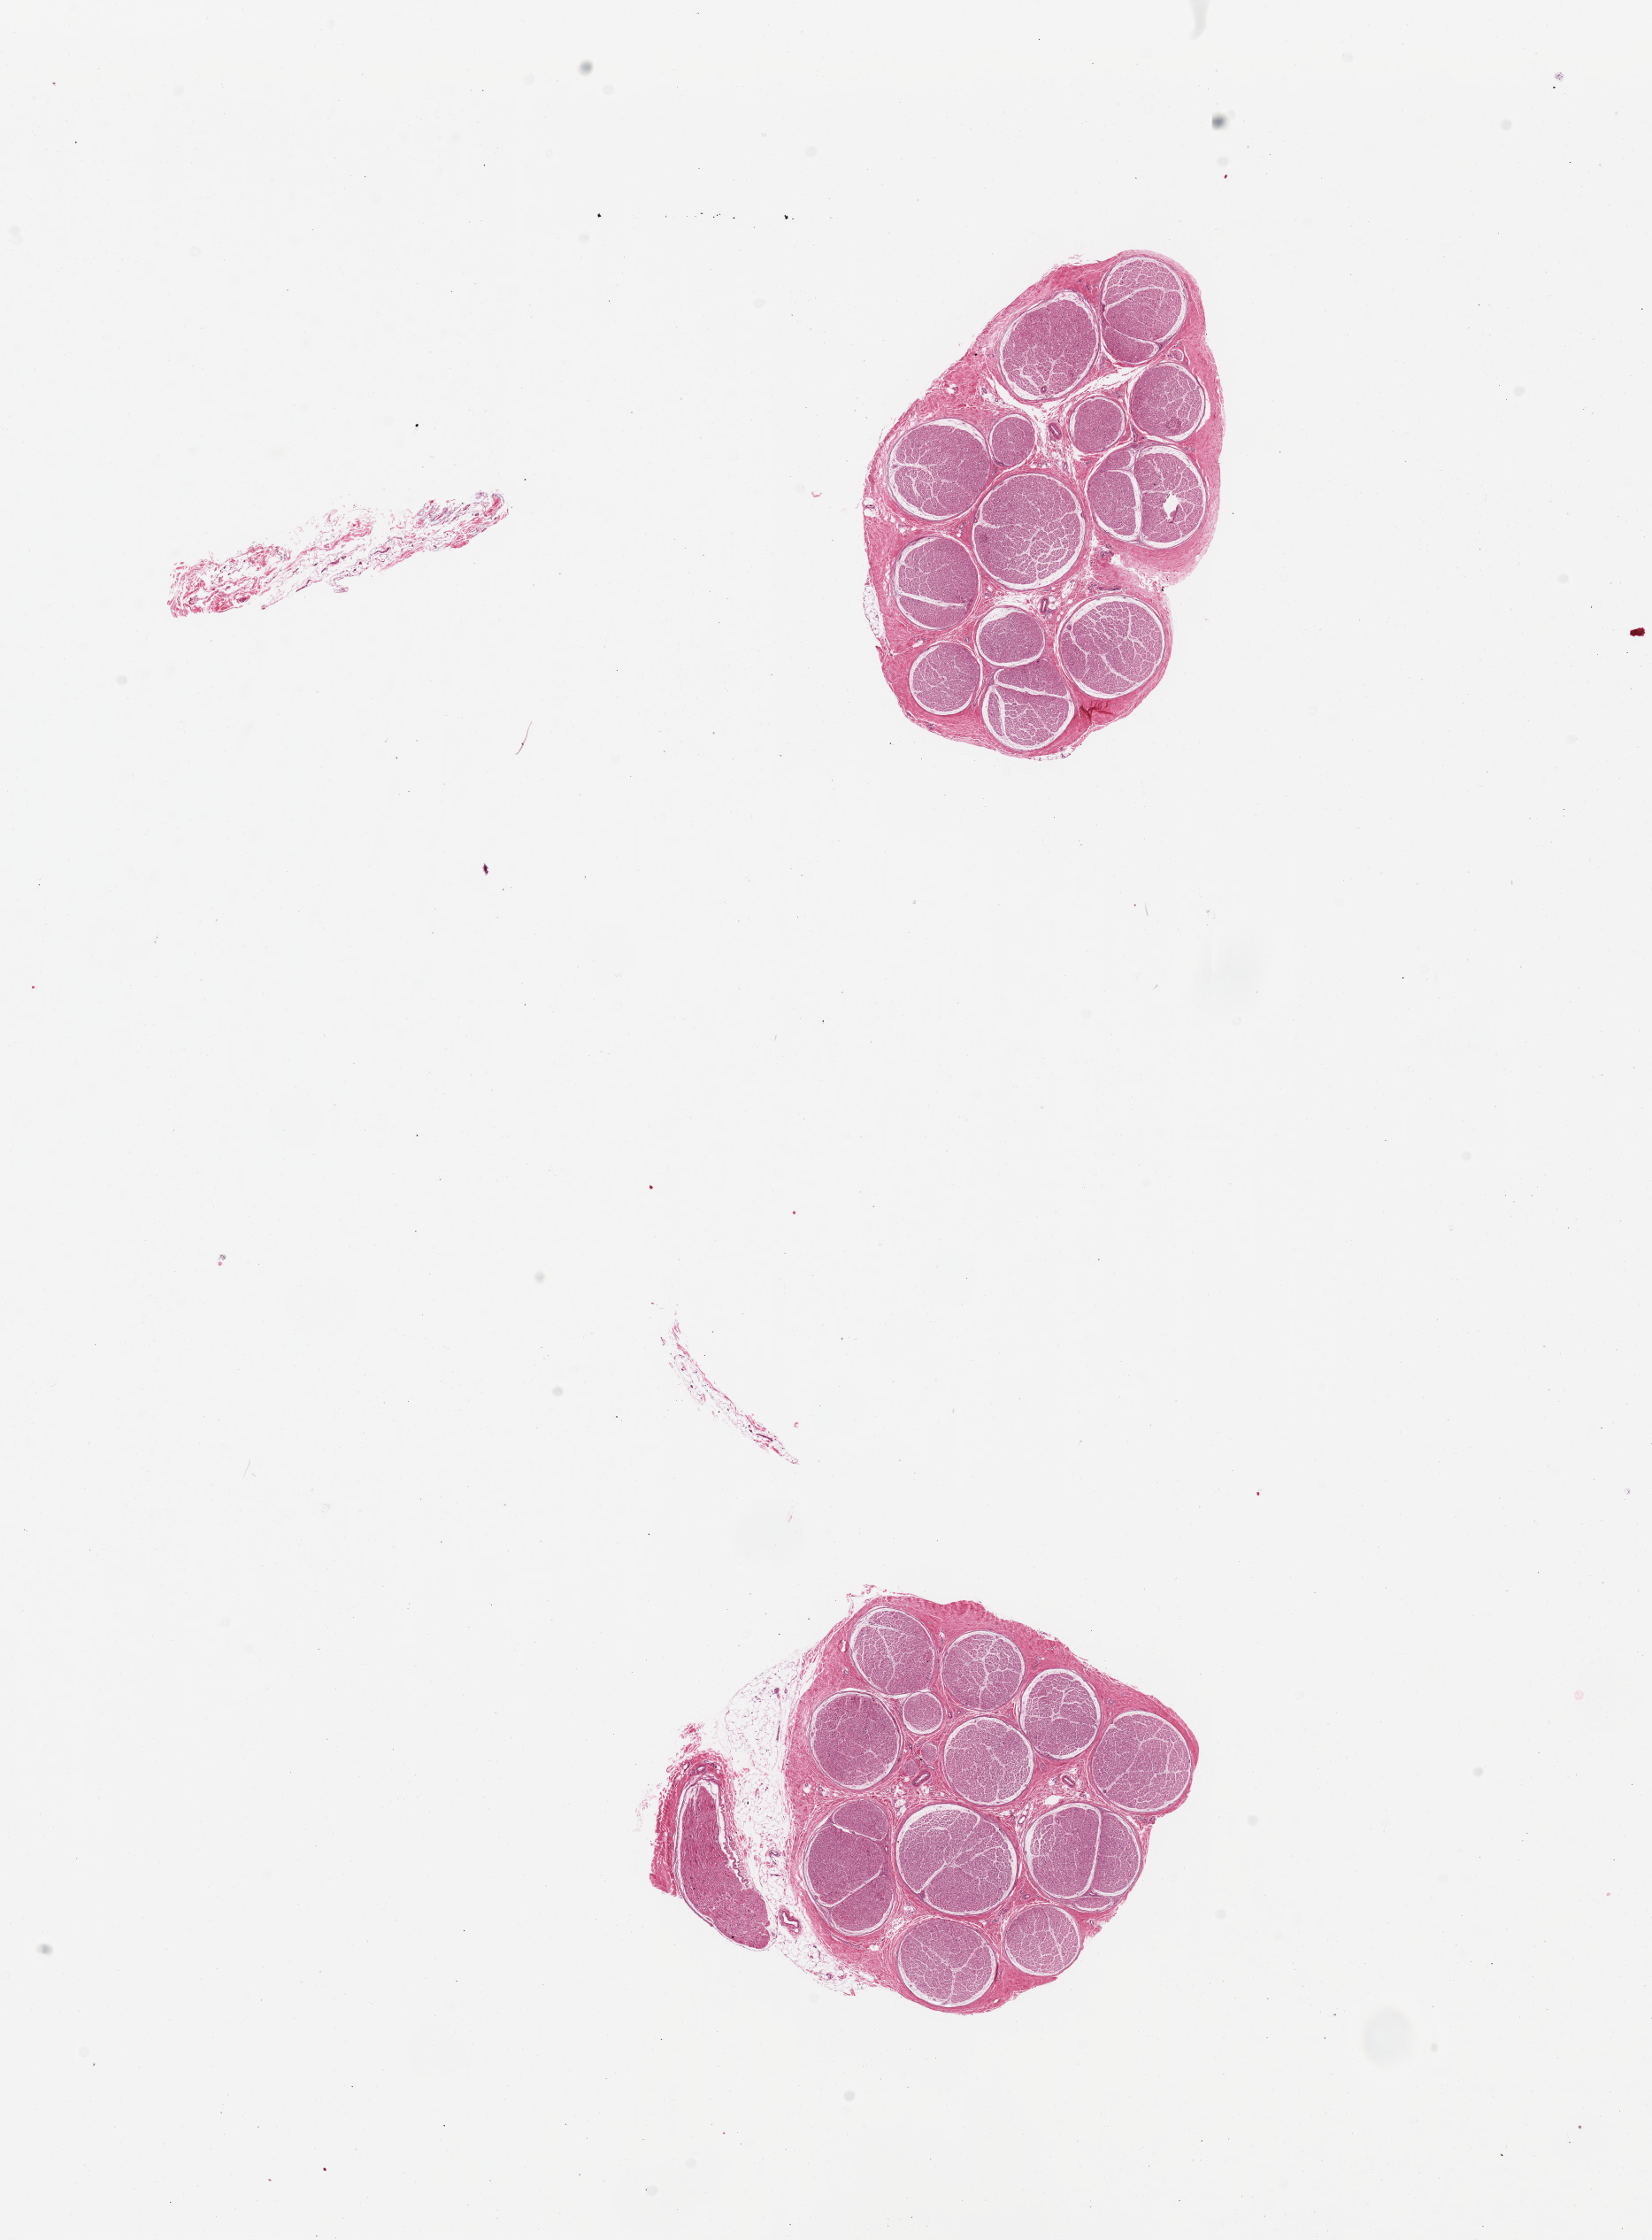
Digitized hematoxylin and eosin (H&E)-stained section — low-resolution overview of the scanned area, about 14.8 x 20.0 mm (acquisition: 20x scan), PAXgene-fixed, paraffin-embedded tissue, section of tibial nerve (target tissue), tissue donor sample. Donor sex: male.
Pathologist's review note for this sample: 2 pieces; nerve and prineurium.